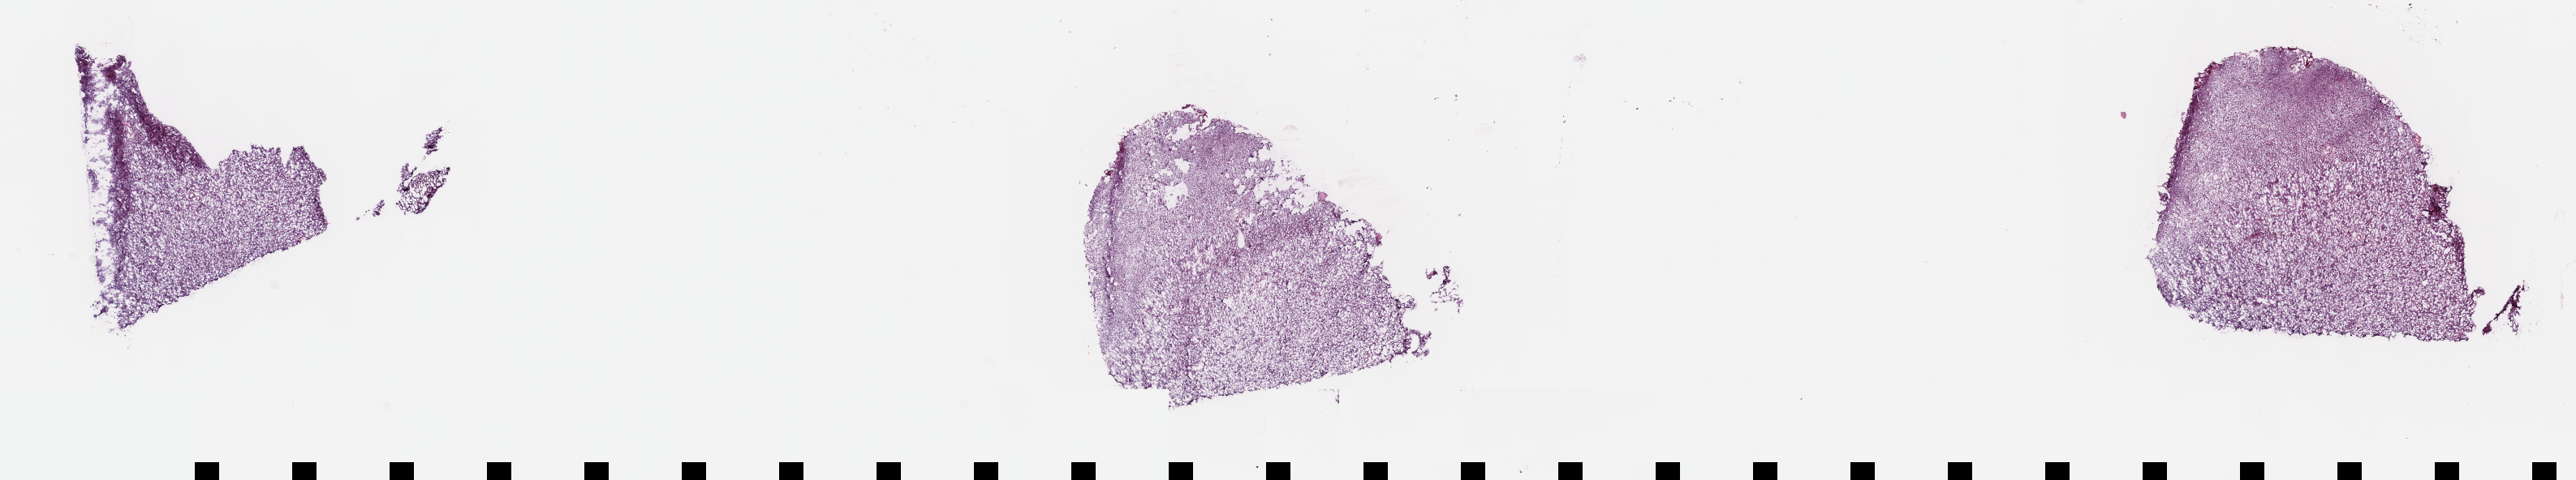
Digitized H&E-stained tissue section (whole slide) — shown as a low-resolution overview of the whole scanned area (about 25.7 x 4.8 mm, slide scanned at 40x), frozen section from the top of the tissue portion, brain, primary tumour sample. Male, age 43 years at initial diagnosis. Histologic grade: G3 (poorly differentiated). Slide review estimates, as recorded: tumour cells 45%, tumour nuclei 85%, normal cells 10%, stromal cells 45%, necrosis 0%. Inflammatory infiltration, as recorded: lymphocyte infiltration 0%, monocyte infiltration 0%, neutrophil infiltration 0%.
Pathologic diagnosis: Astrocytoma, anaplastic (cerebrum). Laterality: right.